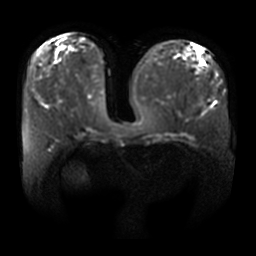
Breast MRI, one axial slice; slice 14 of 36 in the series (ordered by position); diffusion-weighted series; image 2 of 4 stored at this slice position (different b-values; order by instance number); 3 T; 256 × 256 image matrix. Female patient.
Outlined on this slice (outlined manually by an expert reader):
- tumour on diffusion-weighted imaging: box from (x=202, y=62) to (x=205, y=65) px